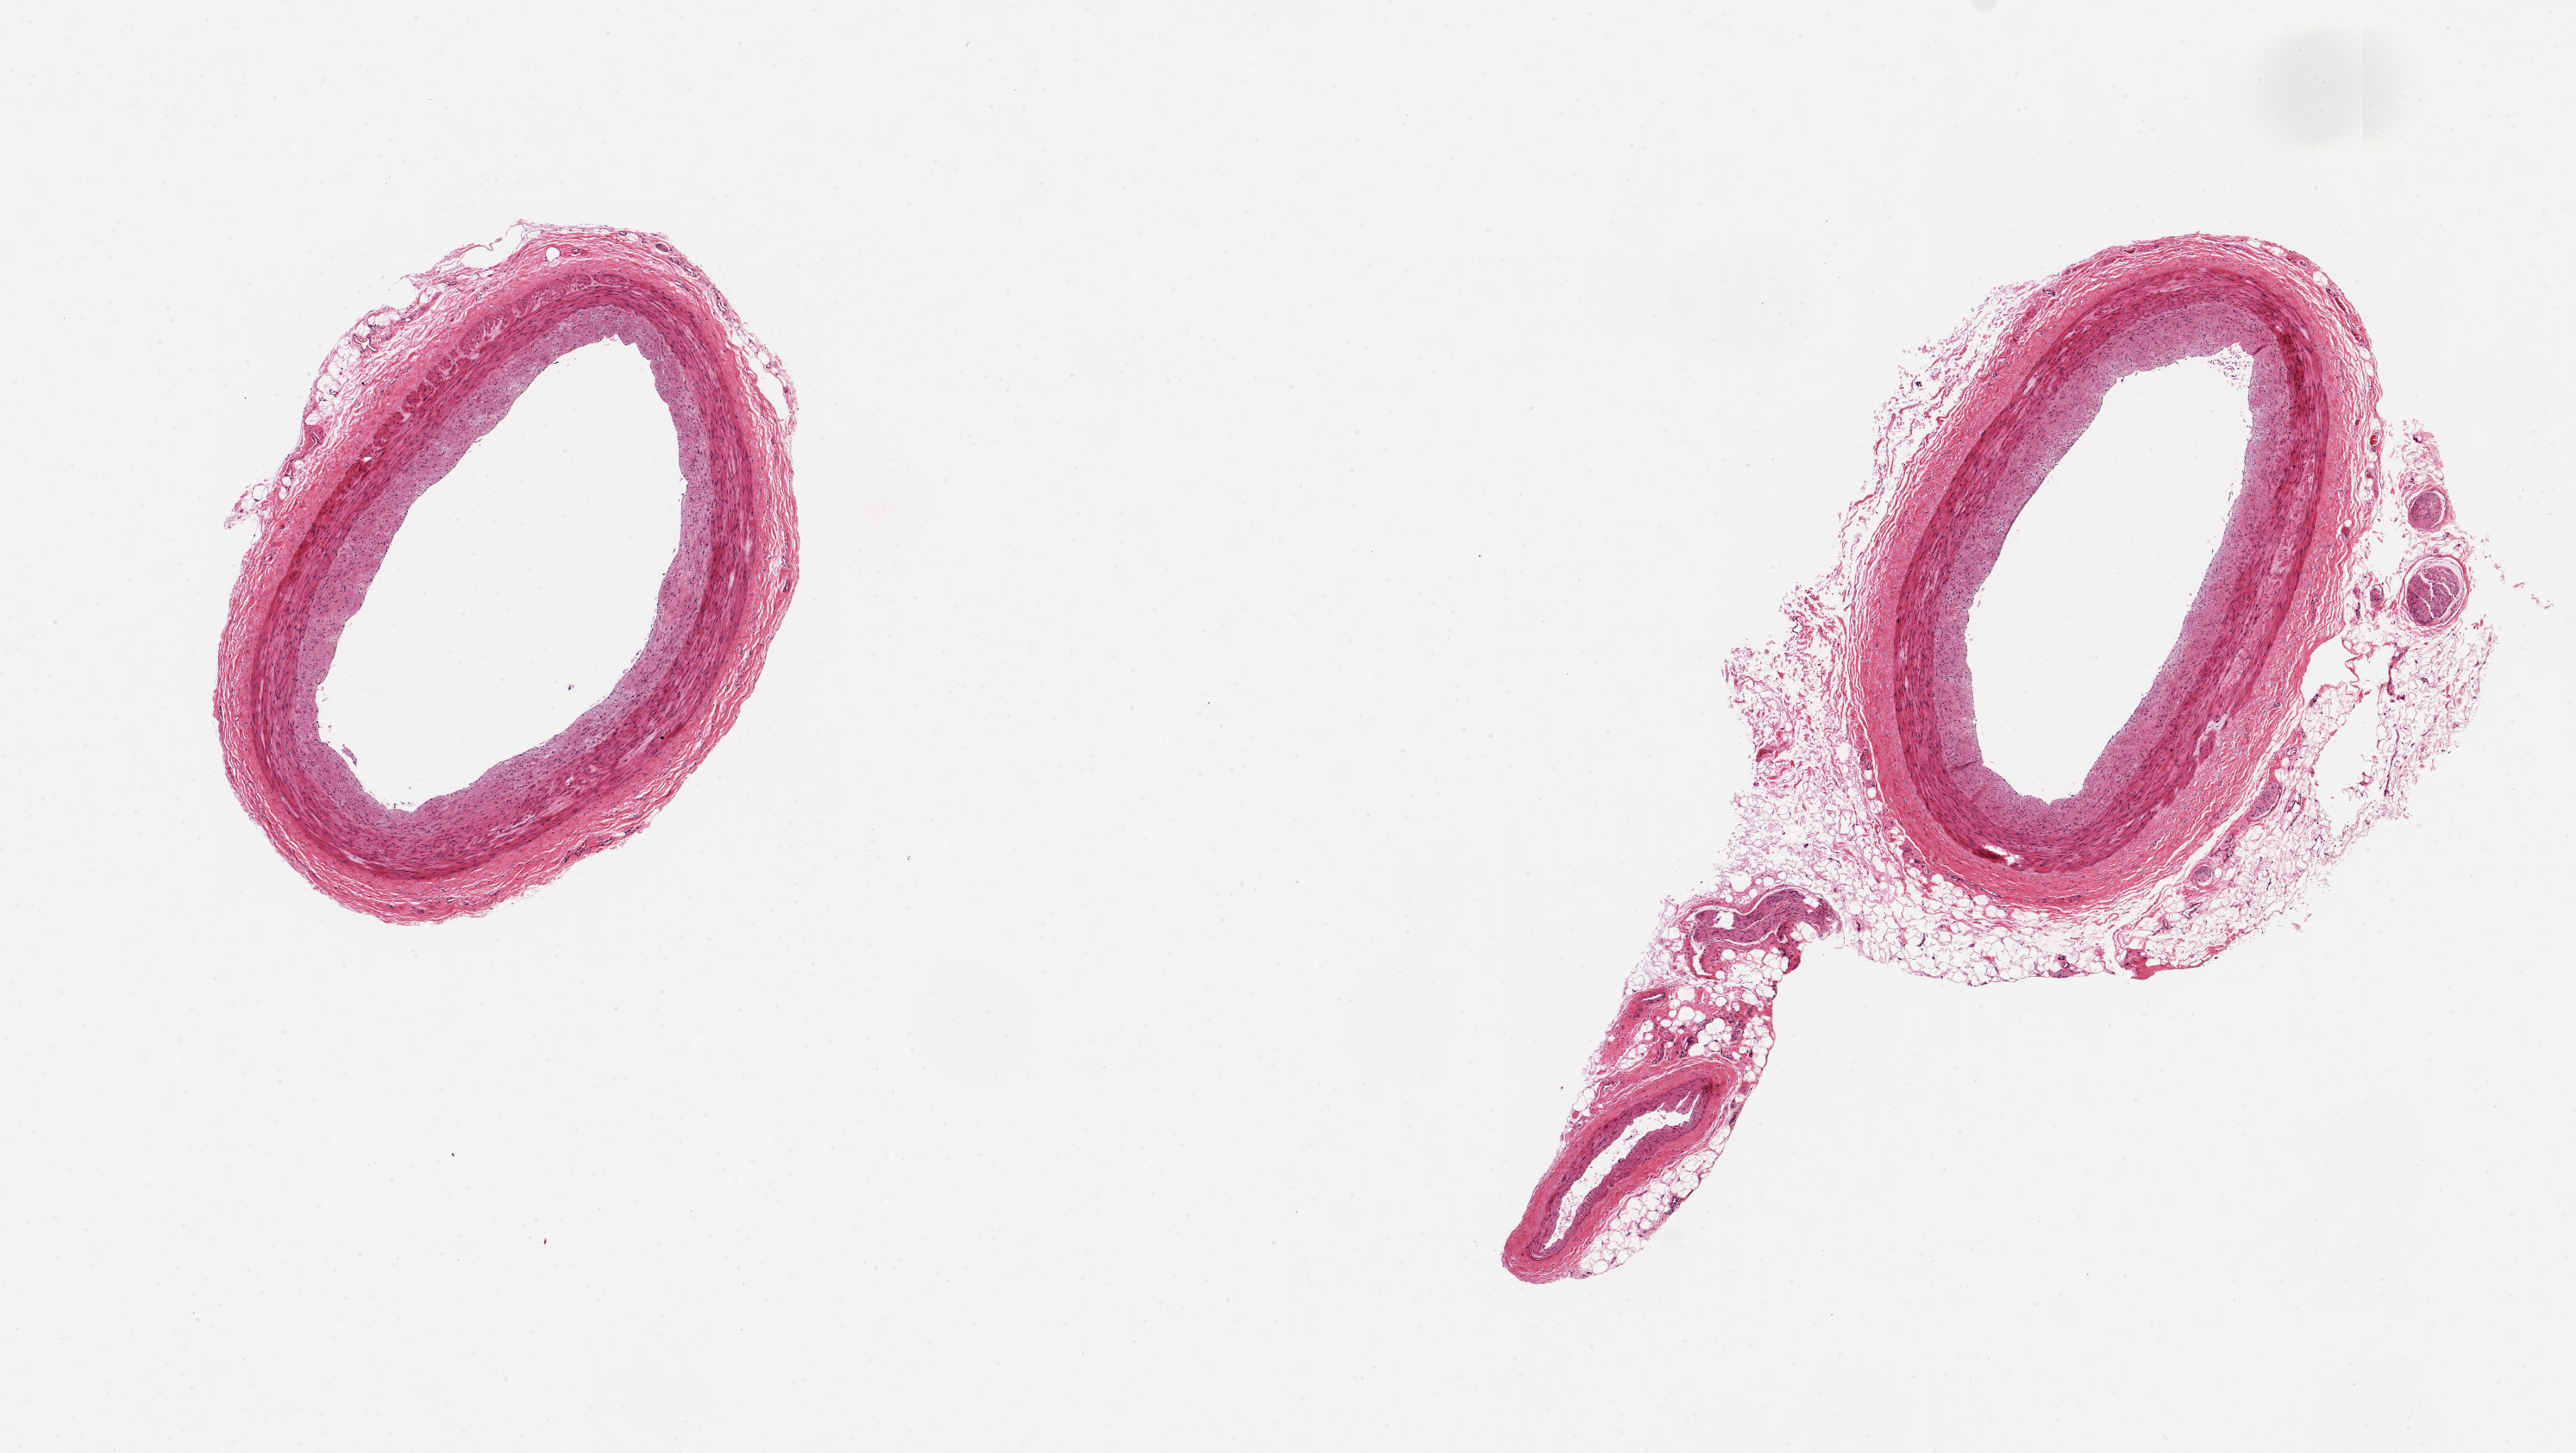
Digitized hematoxylin and eosin (H&E)-stained section — shown as a low-resolution overview of the whole scanned area (about 11.8 x 6.7 mm), PAXgene-fixed paraffin-embedded (PFPE) section, target tissue: coronary artery, donor tissue sample. Donor: male.
Review note (as recorded): 2 ~3.5x2.5mm aliquots, one with partial ~0.5mm rim of fat. Minimal/no atherosclerotic deposition.